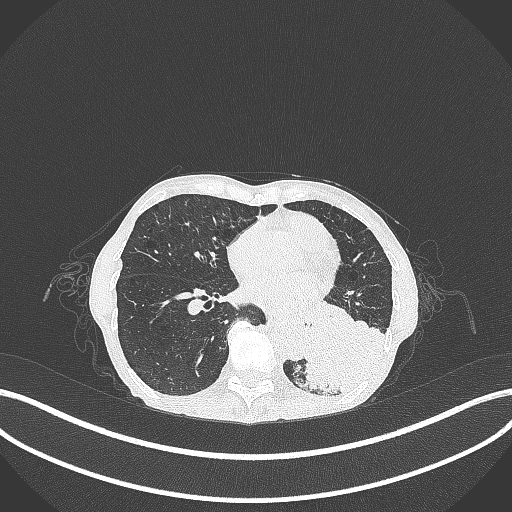
Chest CT, one axial slice. Slice 105 of 347 in the series (ordered by position). Reconstruction kernel B70f. 120 kVp. Lung window (W 1500 / L -600 HU). 512 × 512 image matrix, field of view 400 × 400 mm. Female patient, age 70 years. Case-level facts recorded for this patient, not image findings: clinical TNM (as recorded): T3 N0 M0; histopathological grade: G3.
Outlined on this slice (bounding box drawn by a radiologist):
- lung tumour (recorded histology: small cell carcinoma): box from (x=296, y=304) to (x=390, y=400) px